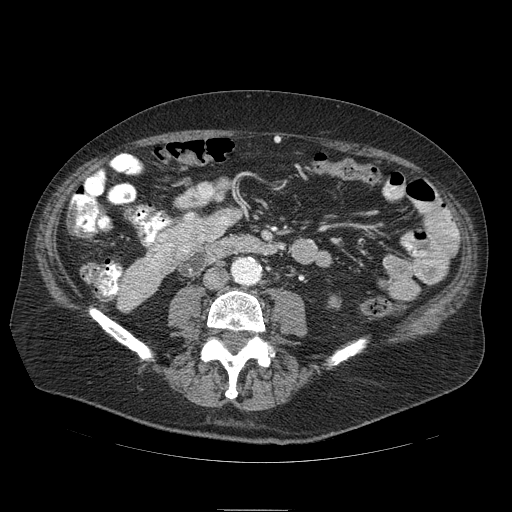
Contrast-enhanced abdominal CT (liver protocol), one axial slice. Slice 10 of 103 in the series (ordered by position). Reconstruction kernel STANDARD. Soft-tissue window (W 400 / L 40 HU). 2.5 mm slice thickness. 512 × 512 image matrix, field of view 440 × 440 mm. From the clinical record (not read from this slice): diagnosis: hepatocellular carcinoma (patient treated with transarterial chemoembolisation; whether this scan precedes or follows treatment is not stated here); TNM stage (as recorded): Stage-IIIA.
Outlined on this slice (semi-automatic segmentation, software-assisted and operator-edited):
- mass: box from (x=148, y=207) to (x=241, y=270) px